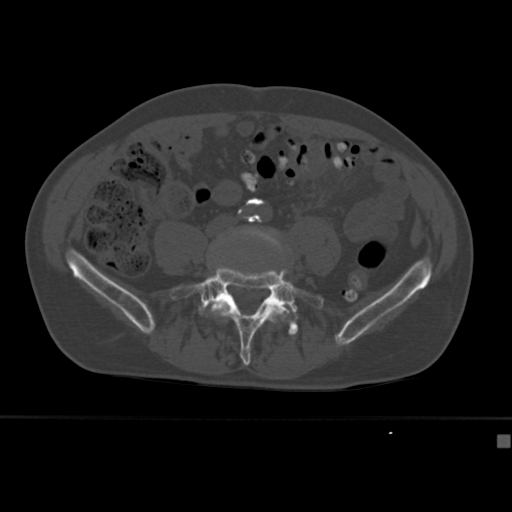
CT including the spine, one axial slice; position 92 of 430 along the scan axis; reconstruction kernel Br40s; bone window (W 1800 / L 400 HU); 1.5 mm slice thickness; 512 × 512 image matrix. Patient: male, 64 years. From the clinical record (not read from this slice): primary cancer: uterus.
Annotated regions visible in this slice (semi-automatically segmented with operator editing):
- L4 vertebra: box from (x=209, y=226) to (x=290, y=321) px
- L5 vertebra: (x=171, y=266)–(x=324, y=366)